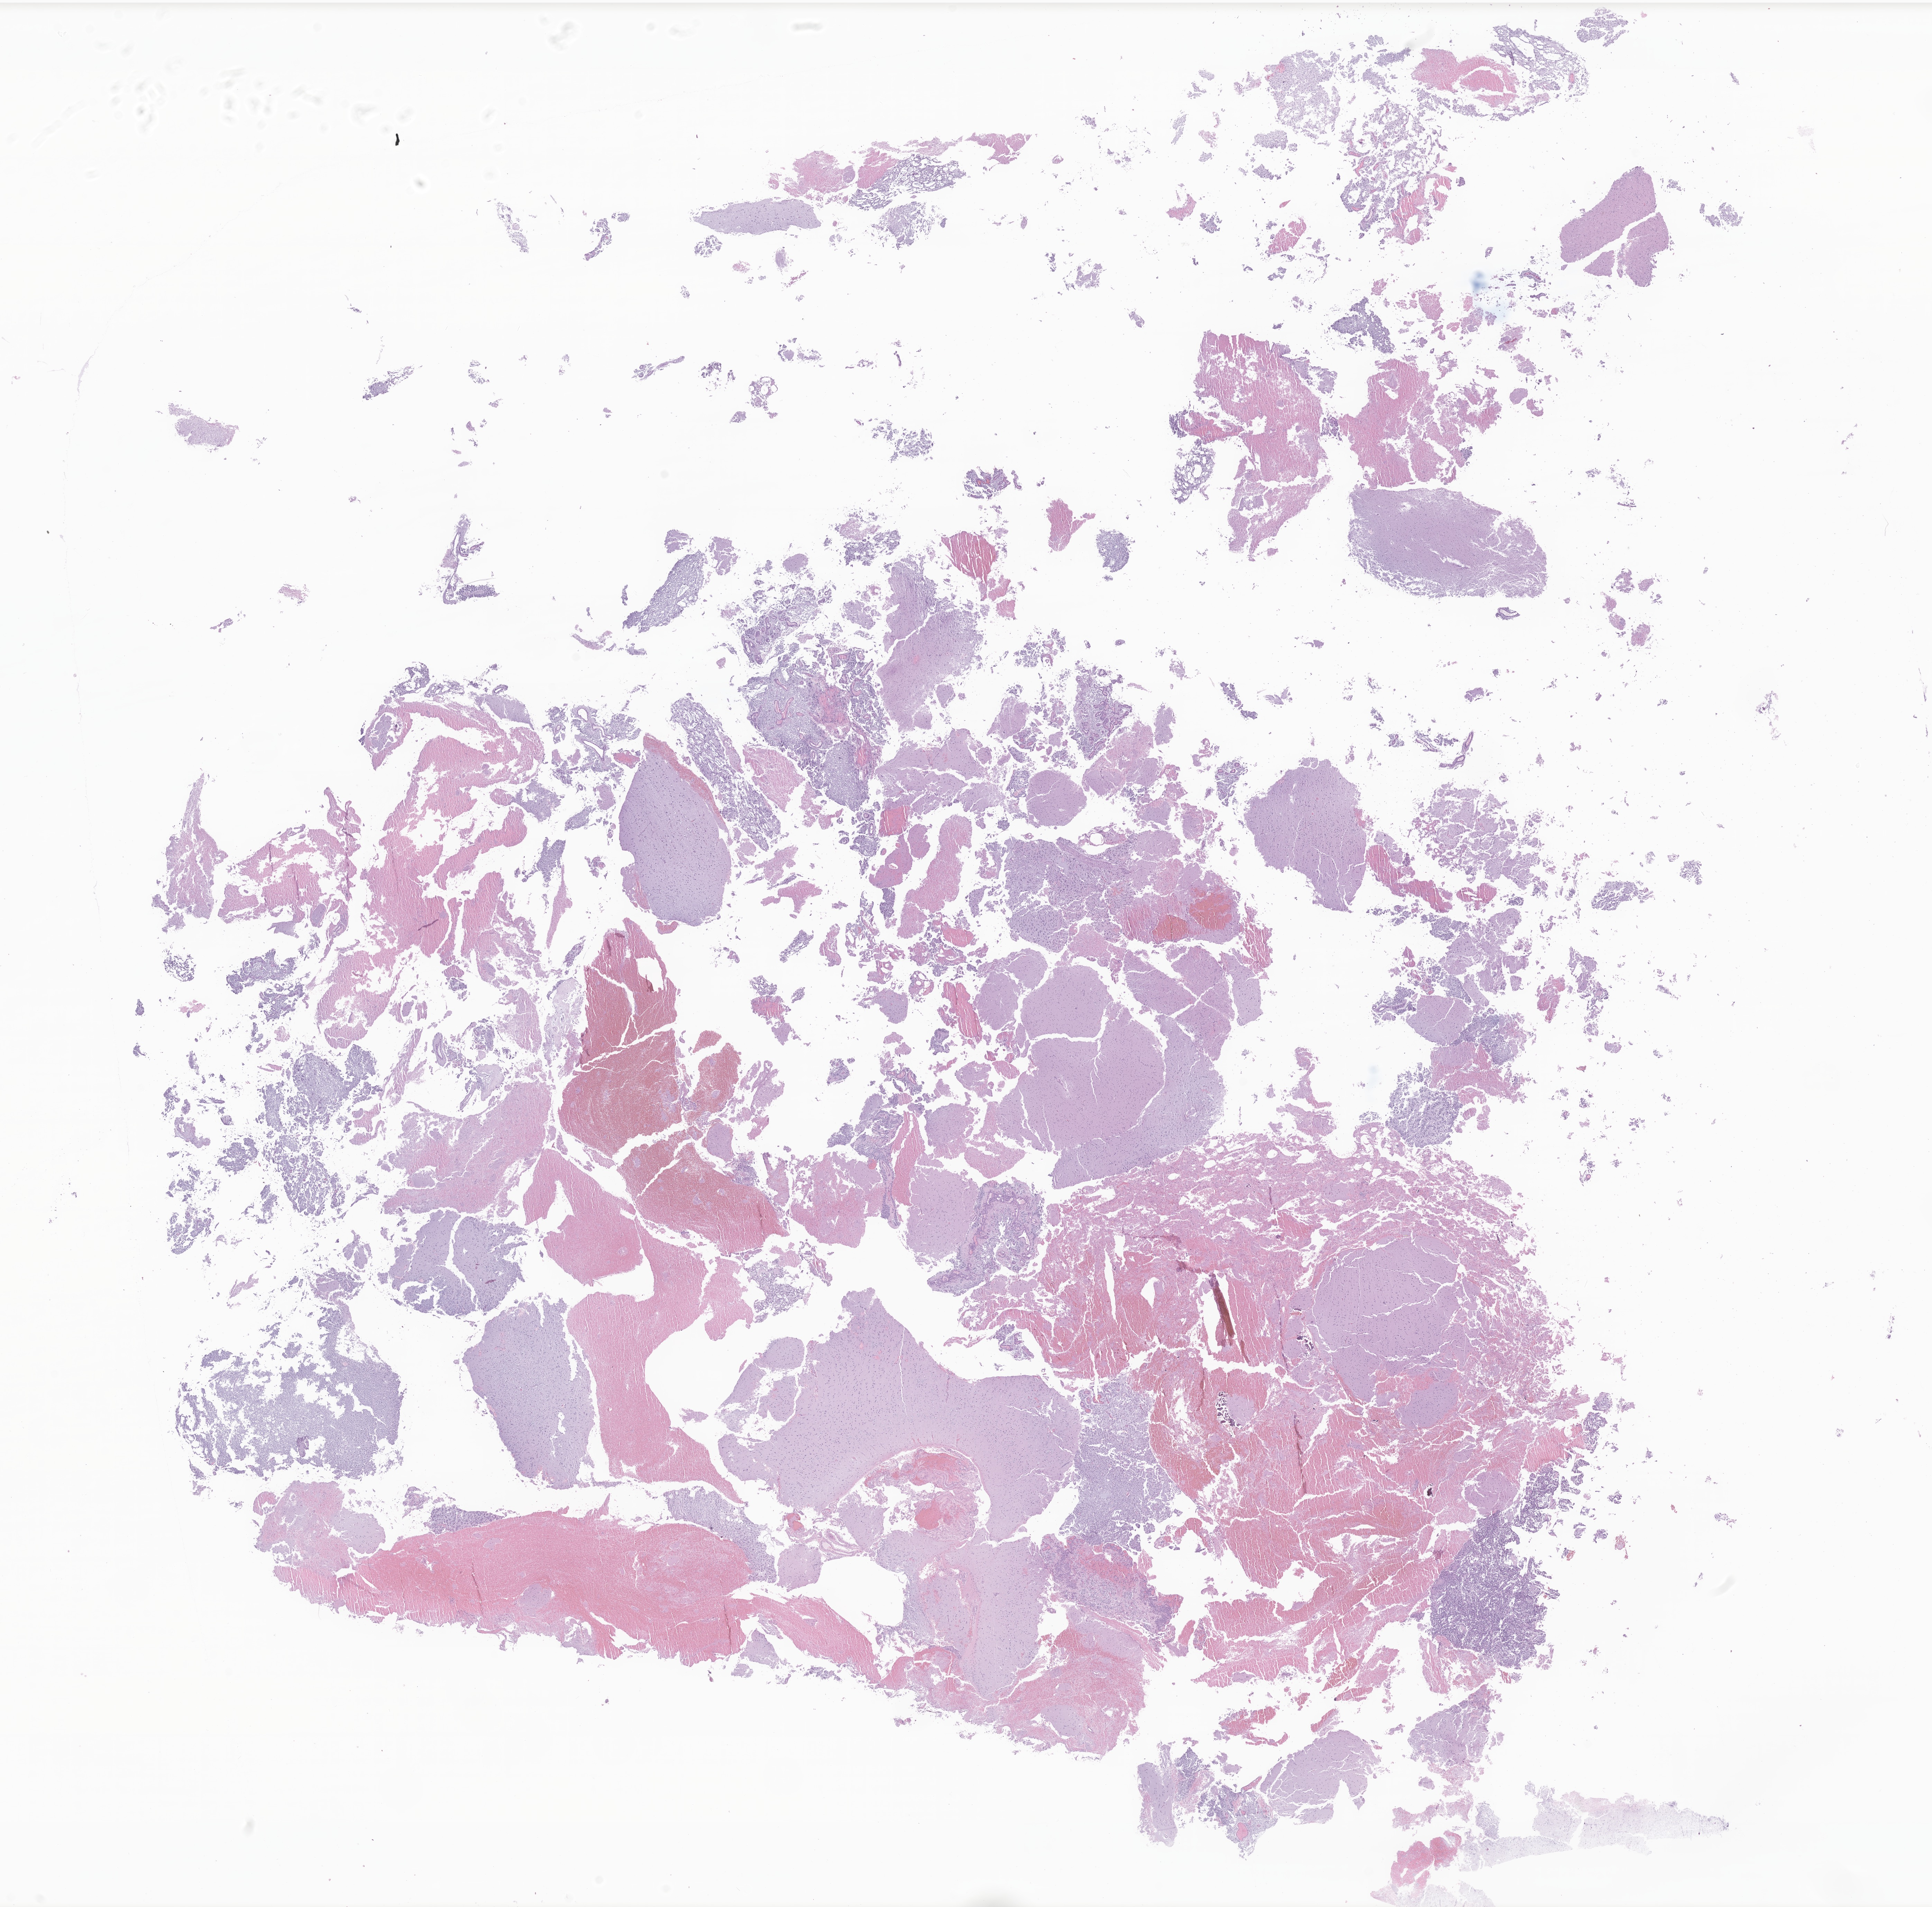
Whole-slide image, haematoxylin and eosin stain of tumor tissue from the brain — a low-resolution overview of the entire scanned area, about 23.5 x 23.2 mm, FFPE section. Patient: female, age 162 months (13 years 6 months).
Diagnosis: Neoplasm, uncertain whether benign or malignant.